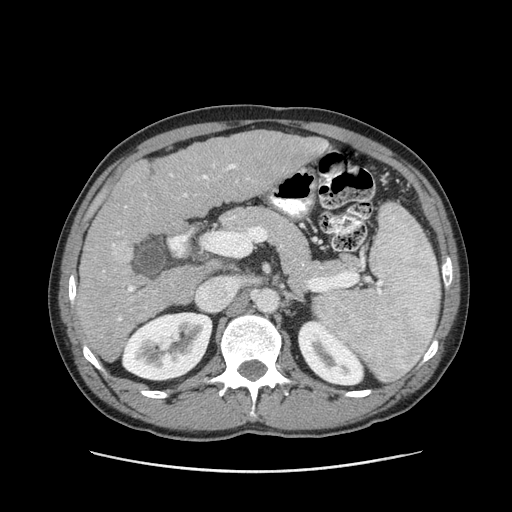
Contrast-enhanced abdominal CT (liver protocol), one axial slice; position 49 of 93 along the scan axis; 120 kVp; soft-tissue window (W 400 / L 40 HU); 2.5 mm slice thickness; 512 × 512 image matrix, field of view 380 × 380 mm. From the clinical record (not read from this slice): diagnosis: hepatocellular carcinoma (patient treated with transarterial chemoembolisation; whether this scan precedes or follows treatment is not stated here); TNM stage (as recorded): Stage-II; Child-Pugh class: A; tumour differentiation: moderately differentiated; tumour nodularity: multinodular.
Annotated regions visible in this slice (semi-automatic segmentation, software-assisted and operator-edited):
- liver parenchyma outside the tumour (the mass and vessels are separate outlines, so this box may not span the whole liver): box from (x=76, y=130) to (x=328, y=362) px
- liver vessels: (x=112, y=144)–(x=328, y=321)